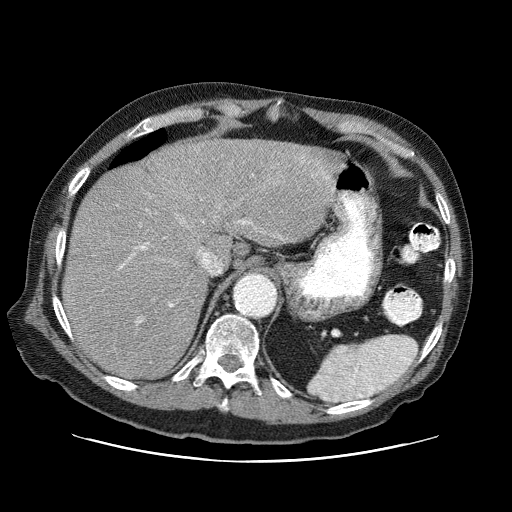
Contrast-enhanced abdominal CT (liver protocol), one axial slice; position 55 of 87 along the scan axis; reconstruction kernel STANDARD; 120 kVp; one of 3 acquisitions stored at this slice position; soft-tissue window (W 400 / L 40 HU); 512 × 512 image matrix, field of view 400 × 400 mm. Case-level facts recorded for this patient, not image findings: diagnosis: hepatocellular carcinoma (patient treated with transarterial chemoembolisation; whether this scan precedes or follows treatment is not stated here); TNM stage (as recorded): Stage-IIIA; Child-Pugh class: A; tumour differentiation: well differentiated; tumour nodularity: multinodular.
Outlined on this slice (semi-automatic segmentation, software-assisted and operator-edited):
- abdominal aorta: bounding box [x1, y1, x2, y2] px = [237, 275, 275, 316]
- liver parenchyma outside the tumour (the mass and vessels are separate outlines, so this box may not span the whole liver): [62, 138, 334, 378]
- liver vessels: [120, 172, 333, 323]